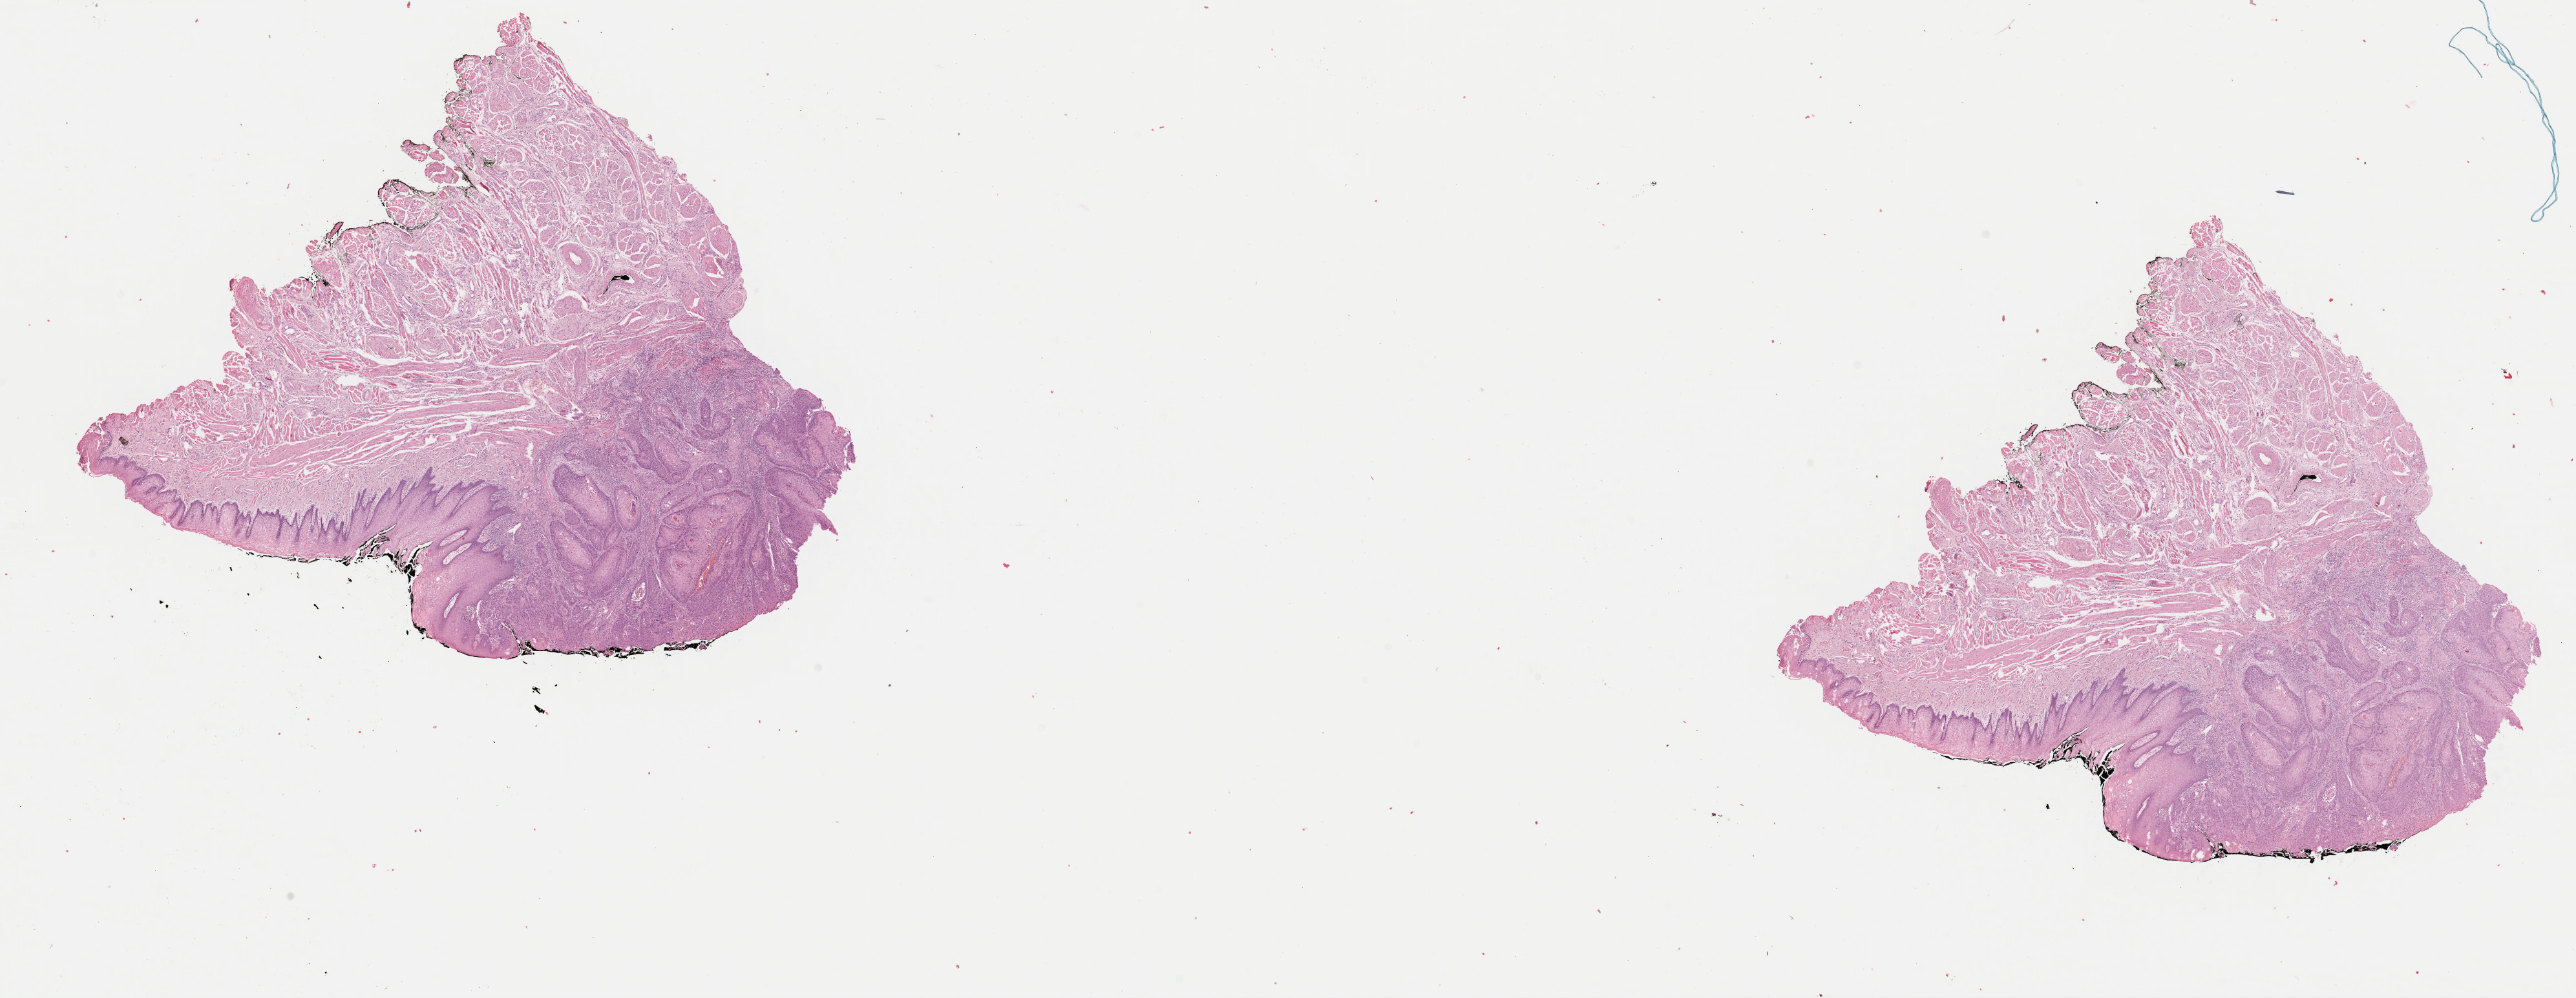
Digitized Hematoxylin and eosin (H&E) stained tissue section (whole slide) — whole scanned area (about 31.5 x 12.2 mm, slide scanned at 40x) shown as a low-resolution overview. Formalin-fixed paraffin-embedded (FFPE) diagnostic section. Sample: primary tumour, head and neck. Male patient; age at initial diagnosis 52 years. Histologic grade: G2 (moderately differentiated).
AJCC pathologic stage: II (7th edition). Histologic diagnosis: Squamous cell carcinoma, keratinizing, NOS.